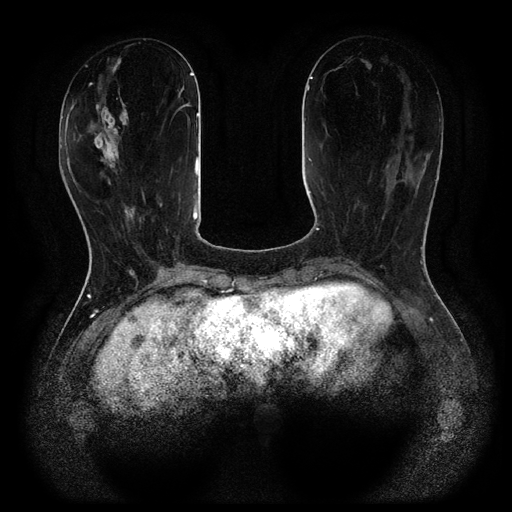
Breast MRI (dynamic contrast-enhanced, multi-phase), one axial slice. Slice 34 of 116 in the series (ordered by position). Dynamic contrast-enhanced series, time point 2 of 5 at this slice position (early post-contrast). 1.5 T. TE 2.6 ms, TR 5.4 ms. 2 mm slice thickness. 512 × 512 image matrix, field of view 340 × 340 mm. Female patient, age 48 years.
Structures marked on this image (semi-automatic segmentation, software-assisted and operator-edited):
- breast lesion (labelled benign in the annotation): bounding box [x1, y1, x2, y2] px = [86, 89, 129, 168]